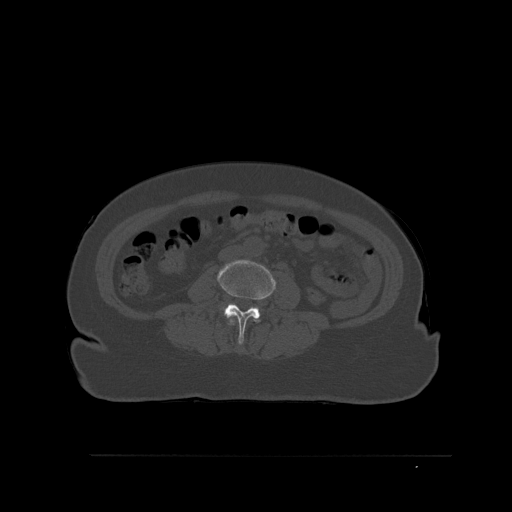
CT including the spine, one axial slice; position 223 of 527 along the scan axis; bone window (W 1800 / L 400 HU); 1.5 mm slice thickness; 512 × 512 image matrix, field of view 470 × 470 mm. Patient: female, 73 years. From the clinical record (not read from this slice): primary cancer: breast; vertebrae with lytic lesions (as recorded): L2.
Outlined on this slice (semi-automatically segmented with operator editing):
- L2 vertebra: bounding box (x1, y1, x2, y2) in pixels: (229, 315, 235, 325)
- L3 vertebra: (217, 260, 276, 344)
- L4 vertebra: (220, 307, 225, 312)